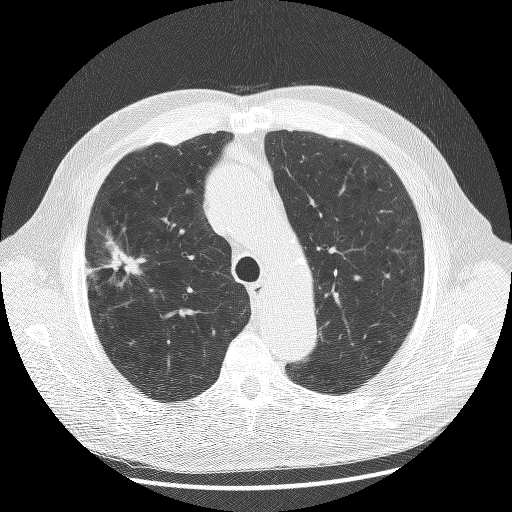
Axial slice from a low-dose chest CT screening exam. First (baseline) screen. Lung window (W 1500 / L -600 HU). Slice 40 of 175 in the series. Male participant, aged 70 years at enrolment. Current smoker at enrolment.
Lesion marked by an expert reader, box from (x=78, y=233) to (x=147, y=305) px. The screening reader recorded 2 non-calcified nodules or masses ≥4 mm on this exam; which of them this box marks is not recorded.